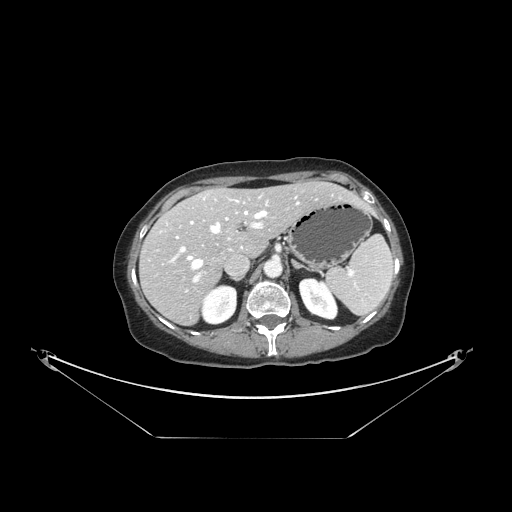
Contrast-enhanced abdominal CT, one axial slice; slice 97 of 148 in the series (ordered by position); reconstruction kernel STANDARD; intravenous contrast given; soft-tissue window (W 400 / L 40 HU); 2.5 mm slice thickness; 512 × 512 image matrix, field of view 500 × 500 mm. Female patient, age 73 years. From the clinical record (not read from this slice): diagnosis: colorectal cancer liver metastases, imaged before liver resection; multiple liver metastases: no; largest metastasis: 1 cm; chemotherapy before resection: yes.
Structures marked on this image (expert manual segmentation):
- hepatic veins: bounding box (x1, y1, x2, y2) in pixels: (188, 197, 299, 269)
- liver: (141, 181, 359, 324)
- planned liver remnant (the part of the liver to remain after resection): (169, 182, 359, 256)
- portal vein (with intrahepatic branches): (171, 204, 268, 283)